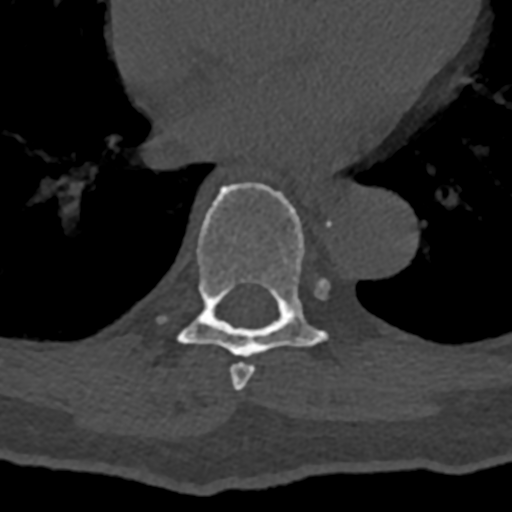
CT including the spine, one axial slice; position 713 of 797 along the scan axis; reconstruction kernel Br40s/3; bone window (W 1800 / L 400 HU); 0.5 mm slice thickness; 512 × 512 image matrix, field of view 160 × 160 mm. Male patient, age 74 years. From the clinical record (not read from this slice): primary cancer: renal.
Outlined on this slice (semi-automatic segmentation, software-assisted and operator-edited):
- T7 vertebra: bounding box <229,363,255,391> (left, top, right, bottom; pixels)
- T8 vertebra: <158,182,326,358>